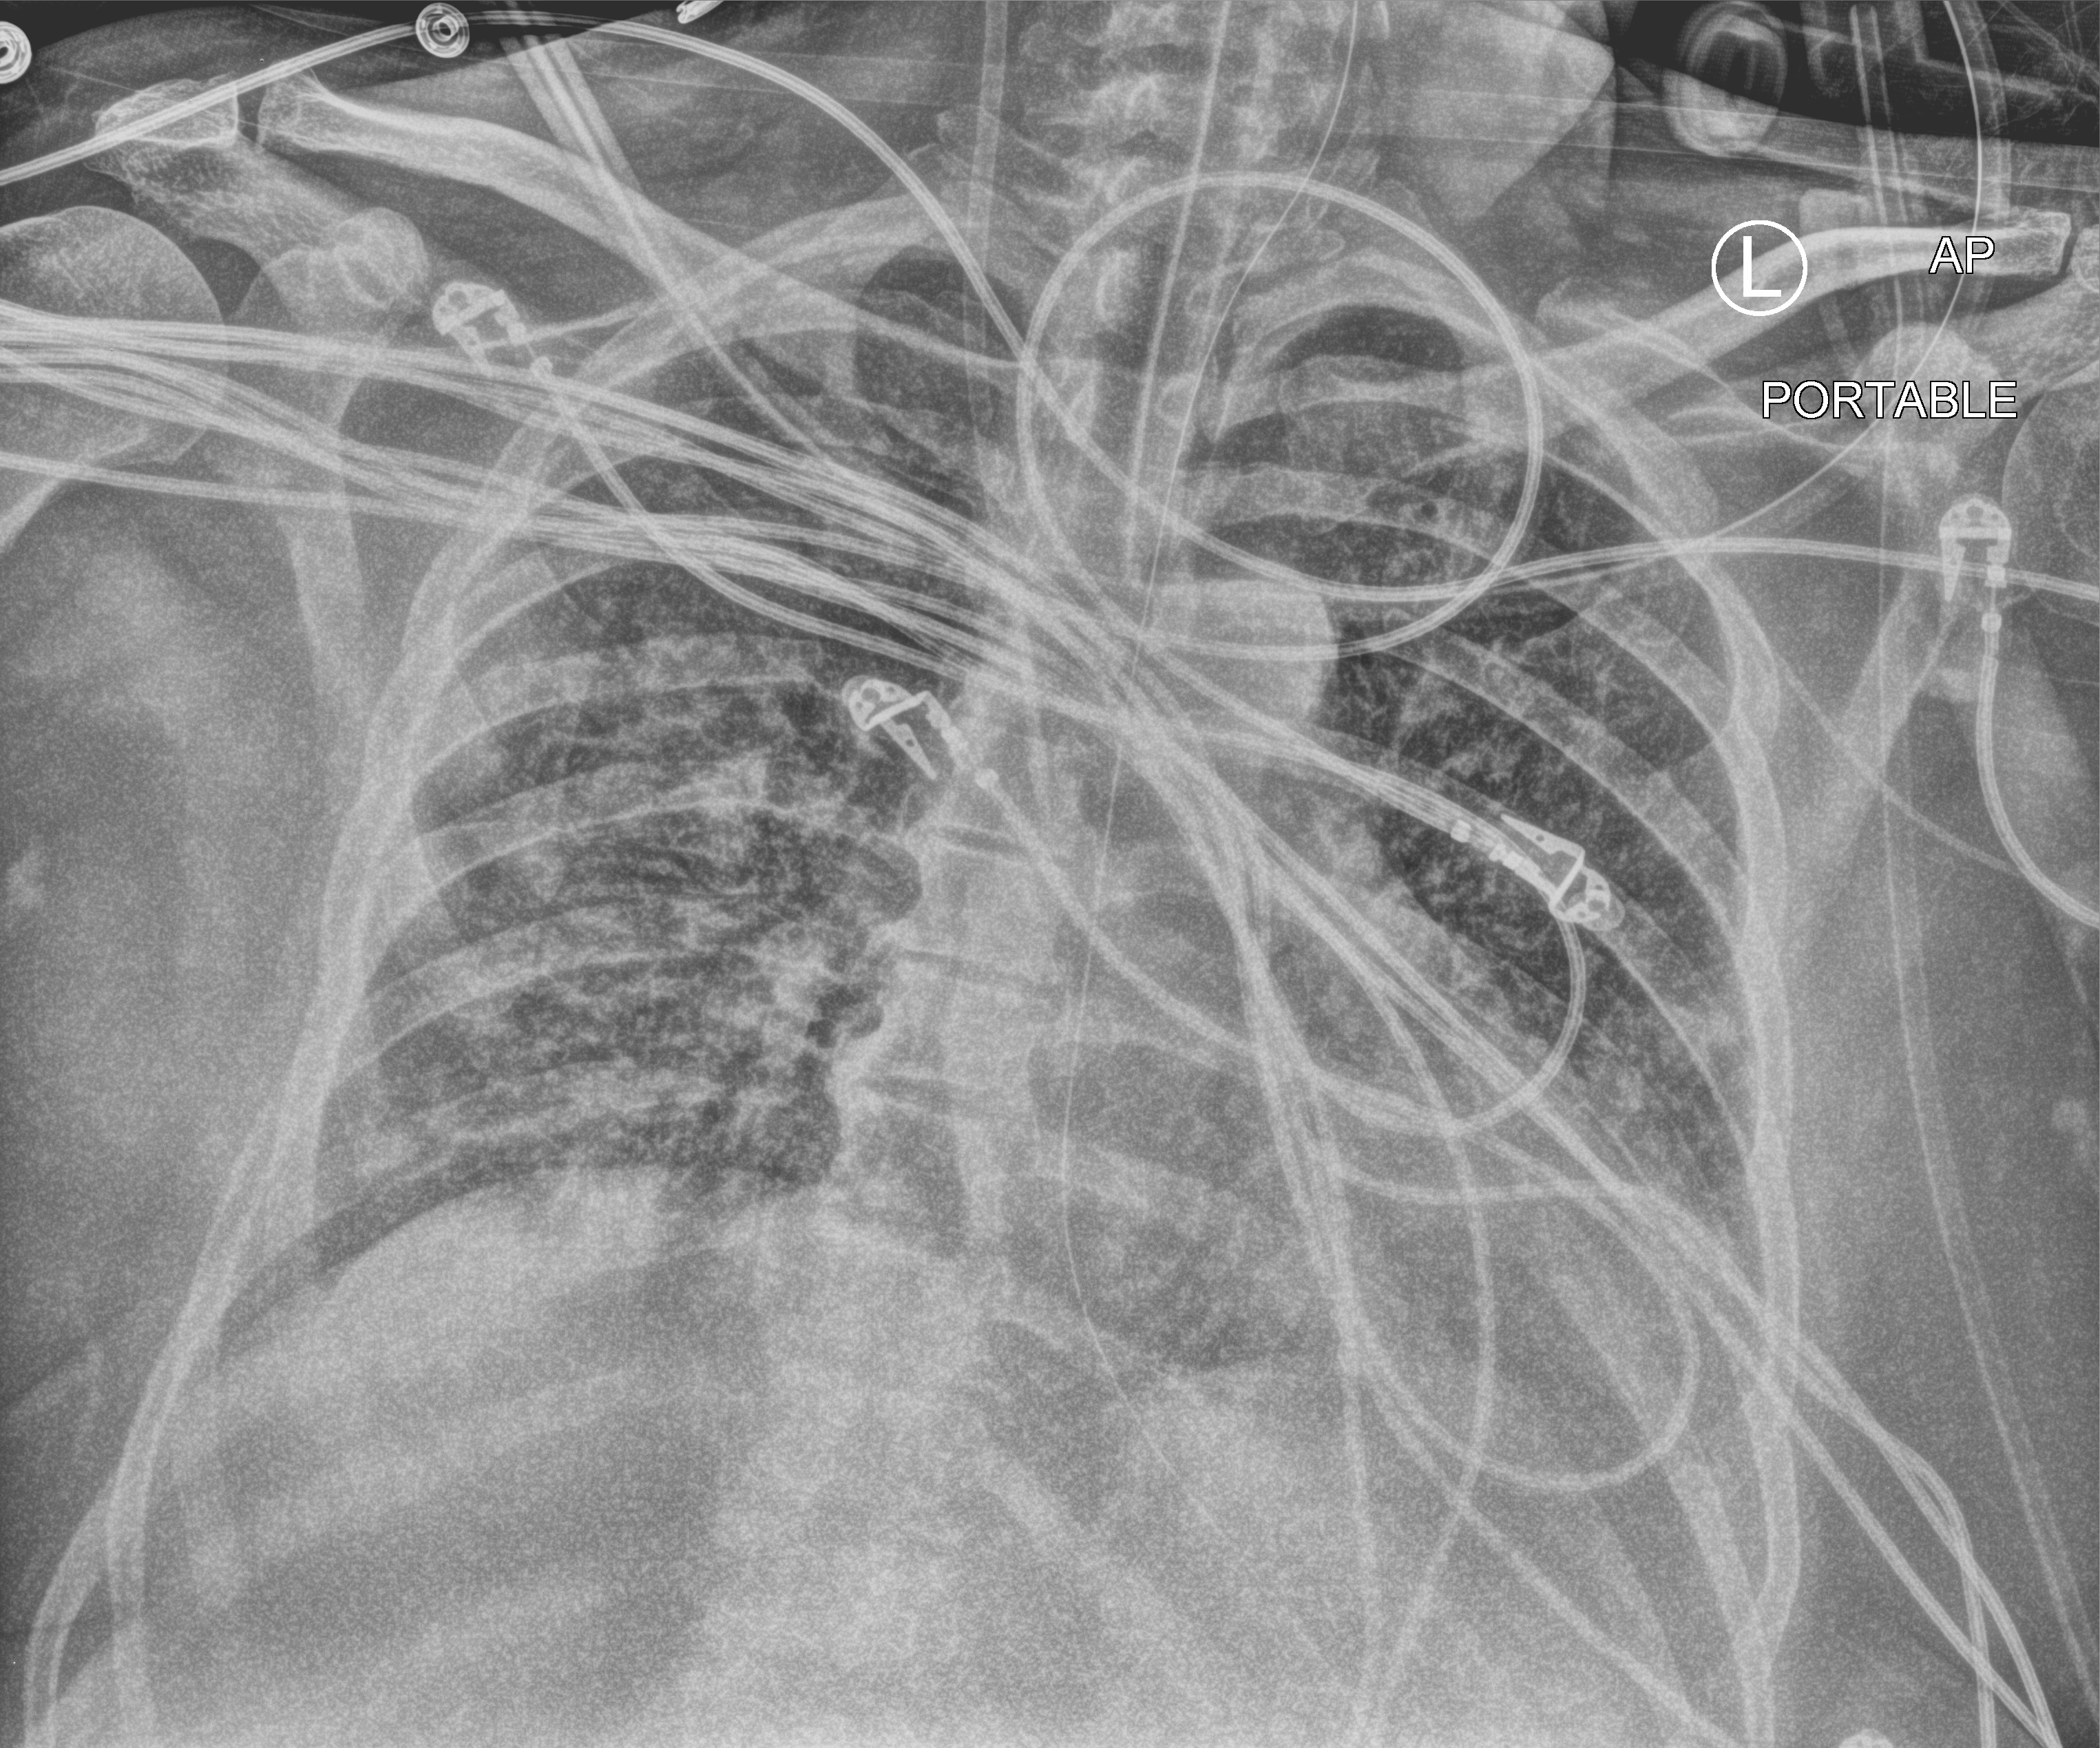
Chest X-ray (portable), anteroposterior (AP) projection. Male patient hospitalised with COVID-19, age 60–74 years.
Admission-level facts for this patient (not findings on this image; timing relative to this image not recorded): mechanically ventilated during this hospital stay: yes; other chronic lung disease (admission record): no.